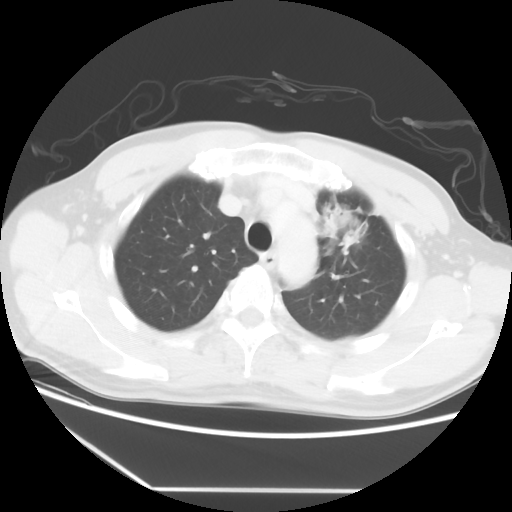
Chest CT, one axial slice; slice 43 of 56 in the series (ordered by position); reconstruction kernel STANDARD; 120 kVp; lung window (W 1500 / L -600 HU); 5 mm slice thickness; 512 × 512 image matrix, field of view 373 × 373 mm. Male patient, age 53 years. From the clinical record (not read from this slice): clinical TNM (as recorded): T2a N1 M1b.
Outlined on this slice (bounding box drawn by a radiologist):
- lung tumour (recorded histology: adenocarcinoma): box from (x=322, y=205) to (x=368, y=257) px